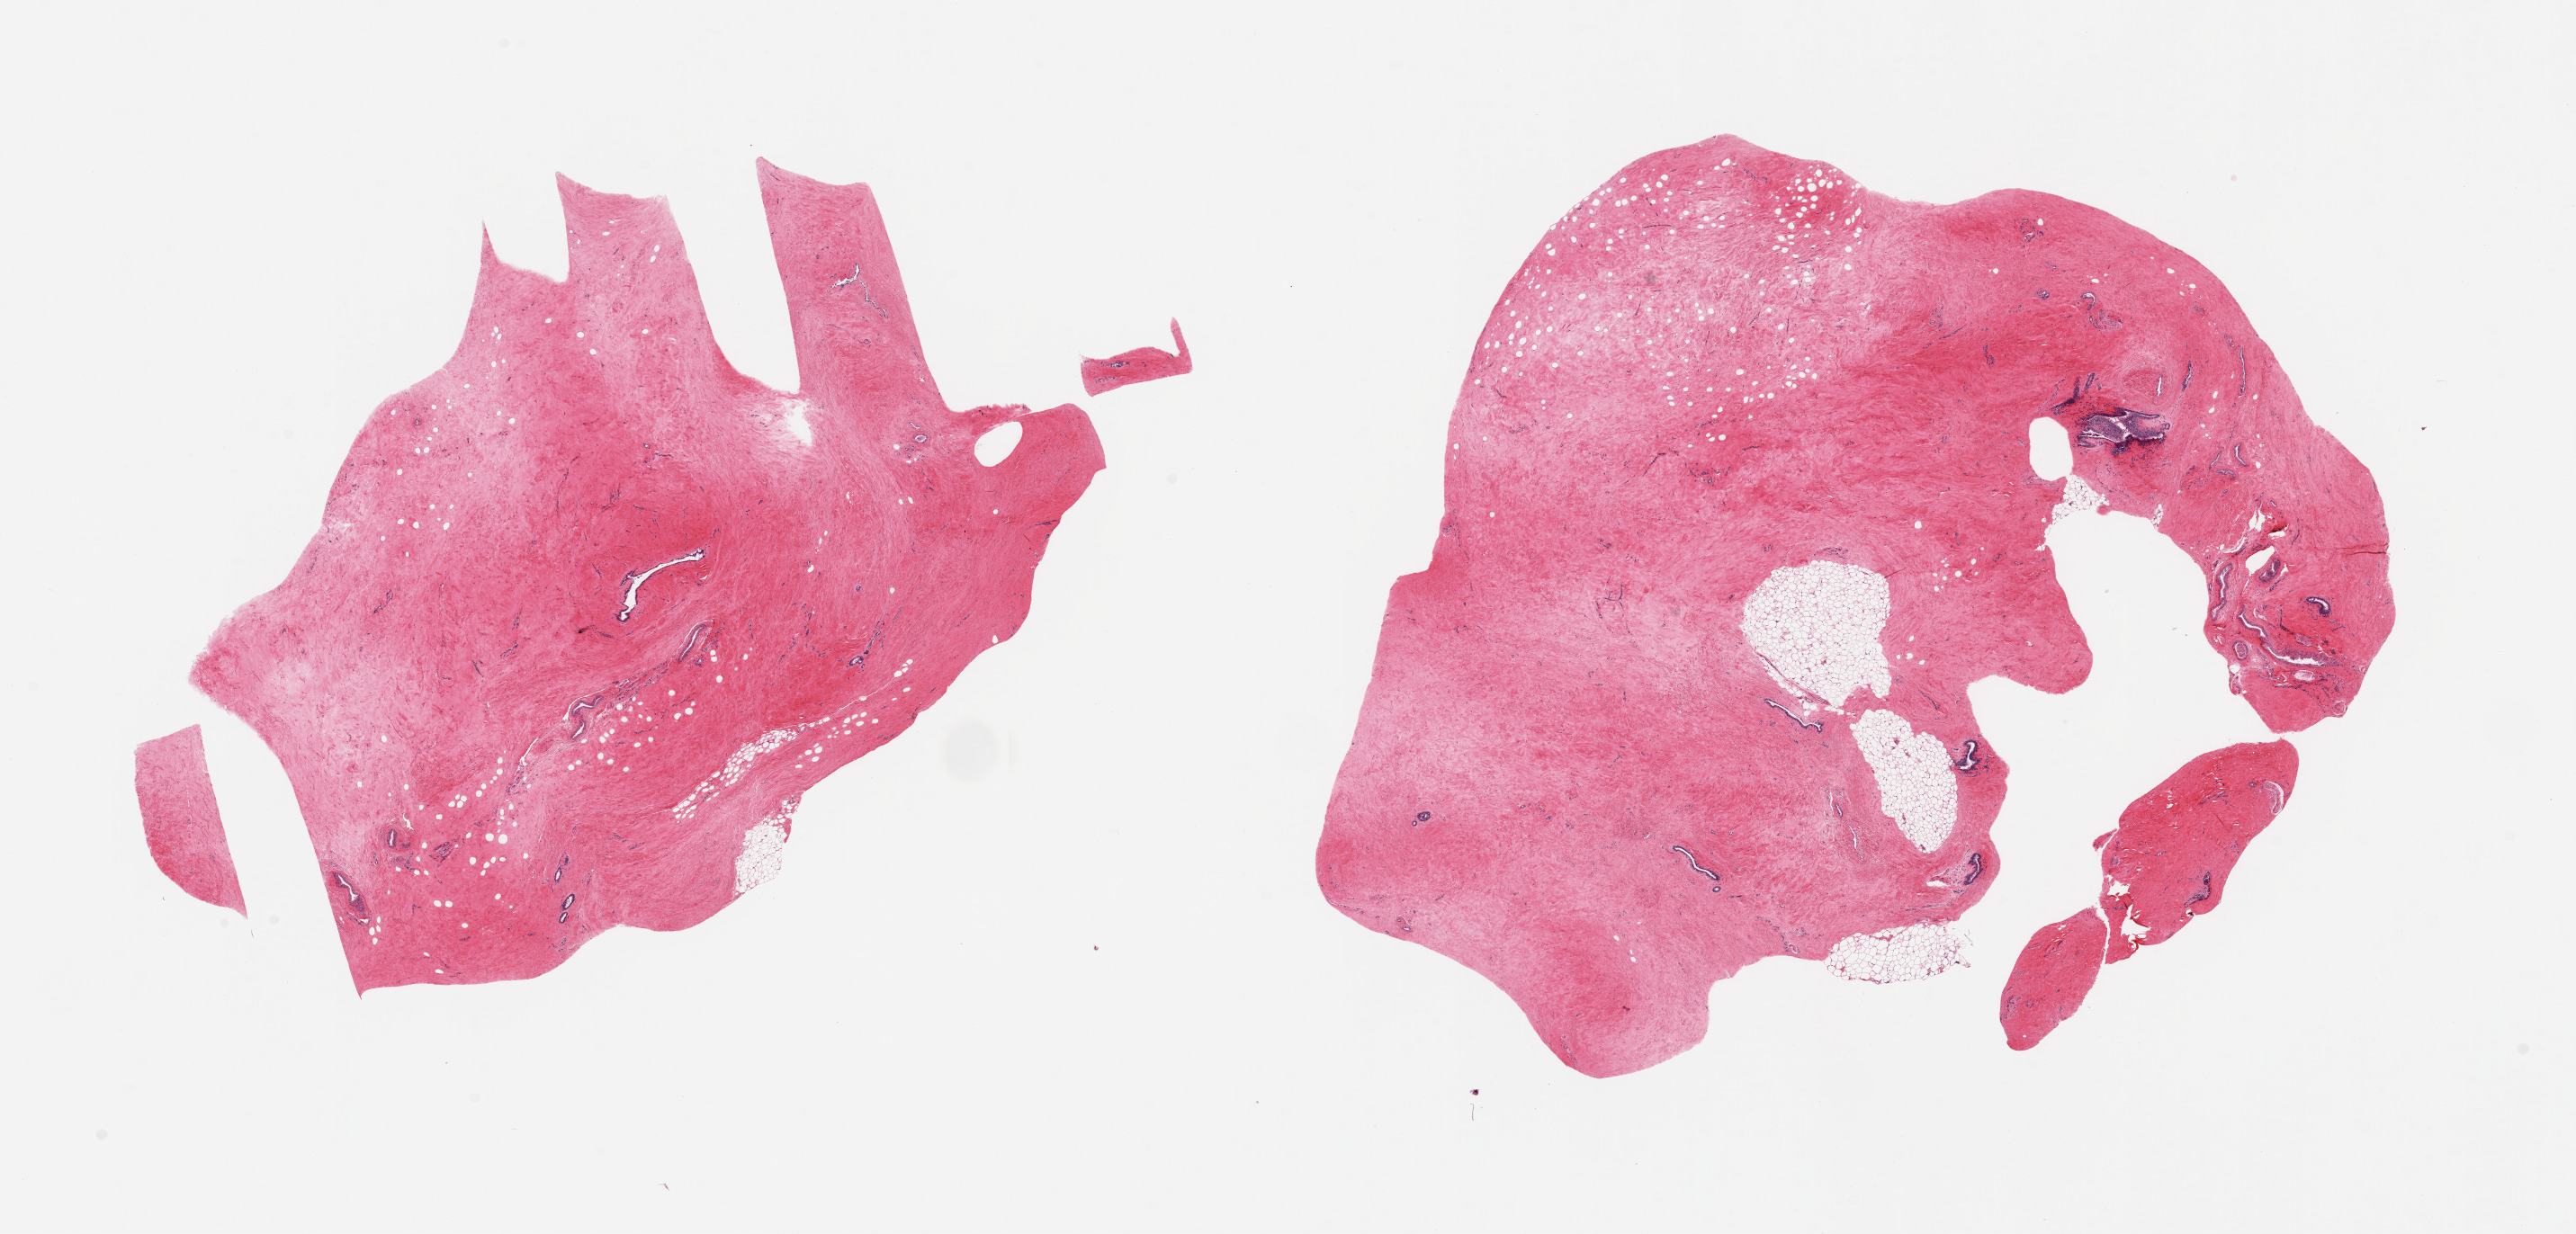
Digitized haematoxylin and eosin-stained section, brightfield — a low-resolution overview of the entire scanned area, about 22.6 x 10.9 mm (slide scanned at 20x). PAXgene-fixed, paraffin-embedded tissue. Section of breast (target tissue). Tissue donor sample. Male donor.
• pathologist's review note for this sample: 2 pieces; dense fibrocollagenous stroma with scattered ducts, small portion of fat